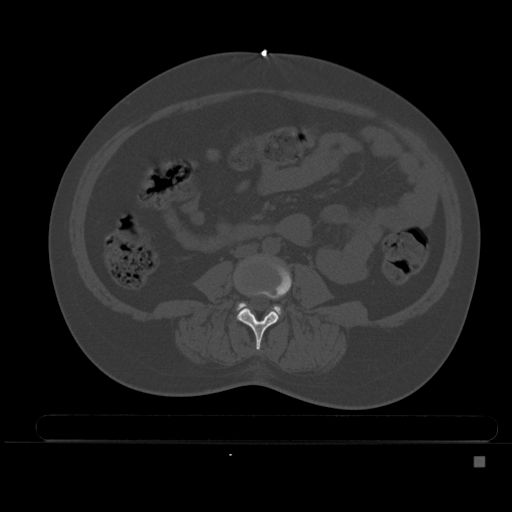
CT including the spine, one axial slice; position 143 of 495 along the scan axis; bone window (W 1800 / L 400 HU); 1.5 mm slice thickness; 512 × 512 image matrix, field of view 404 × 404 mm. Female patient, age 33 years. From the clinical record (not read from this slice): primary cancer: breast; vertebrae with lytic lesions (as recorded): T1.
Outlined on this slice (semi-automatically segmented with operator editing):
- L3 vertebra: bounding box [x1, y1, x2, y2] px = [238, 259, 292, 350]
- L4 vertebra: [238, 303, 281, 313]